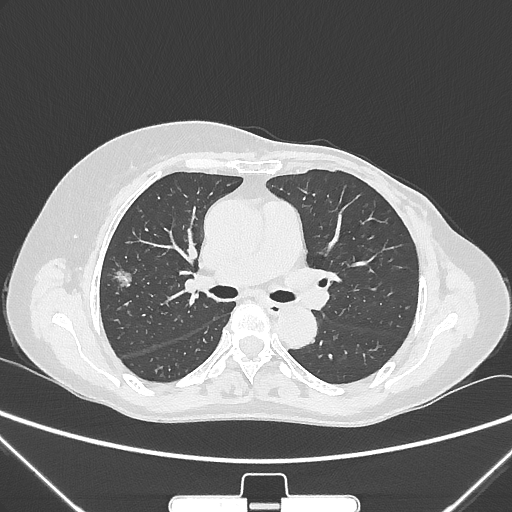
Chest CT, one axial slice; slice 154 of 265 in the series (ordered by position); lung window (W 1500 / L -600 HU); 1 mm slice thickness; 512 × 512 image matrix, field of view 350 × 350 mm. Patient: female, 64 years. Case-level facts recorded for this patient, not image findings: clinical TNM (as recorded): T1c N0 M0.
Outlined on this slice (bounding box drawn by a radiologist):
- lung tumour (recorded histology: adenocarcinoma): bounding box [x1, y1, x2, y2] px = [107, 261, 136, 292]